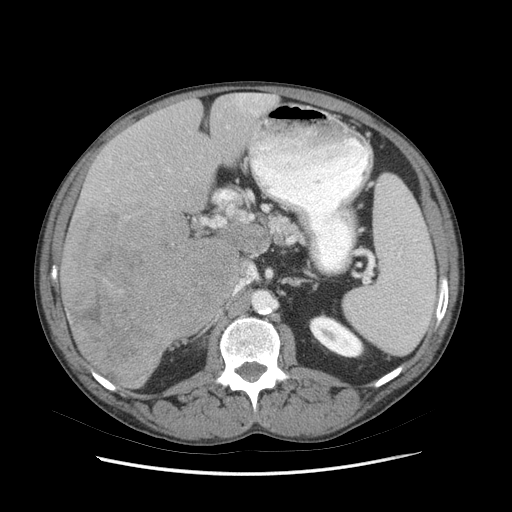
Contrast-enhanced abdominal CT (liver protocol), one axial slice; slice 40 of 89 in the series (ordered by position); 140 kVp; soft-tissue window (W 400 / L 40 HU); 2.5 mm slice thickness; 512 × 512 image matrix, field of view 380 × 380 mm. Case-level facts recorded for this patient, not image findings: diagnosis: hepatocellular carcinoma (patient treated with transarterial chemoembolisation; whether this scan precedes or follows treatment is not stated here); TNM stage (as recorded): Stage-IIIB; Child-Pugh class: A.
Outlined on this slice (semi-automatically segmented with operator editing):
- liver parenchyma outside the tumour (the mass and vessels are separate outlines, so this box may not span the whole liver): bounding box [x1, y1, x2, y2] px = [60, 92, 278, 388]
- mass: [60, 207, 237, 386]
- liver vessels: [108, 94, 264, 226]